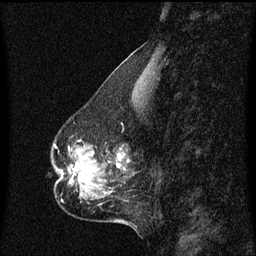
Breast MRI (dynamic contrast-enhanced), one sagittal slice. Slice 23 of 60 in the series (ordered by position). Dynamic contrast-enhanced series, image 2 of 3 at this slice position (ordered by acquisition). 1.5 T. TE 4.2 ms, TR 8.4 ms. 2 mm slice thickness. 256 × 256 image matrix. Female patient, age 50 years. From the clinical record (not read from this slice): setting: breast cancer imaged before/during neoadjuvant chemotherapy; receptor status: HR-positive, HER2-negative.
Structures marked on this image (semi-automatic segmentation, software-assisted and operator-edited):
- analysis volume of interest (the breast-tissue region the enhancement analysis was run in; not a lesion): box from (x=55, y=144) to (x=129, y=191) px
- tumour enhancement mask (voxels above the 70 % enhancement threshold inside the analysis volume of interest): (x=69, y=156)–(x=123, y=183)